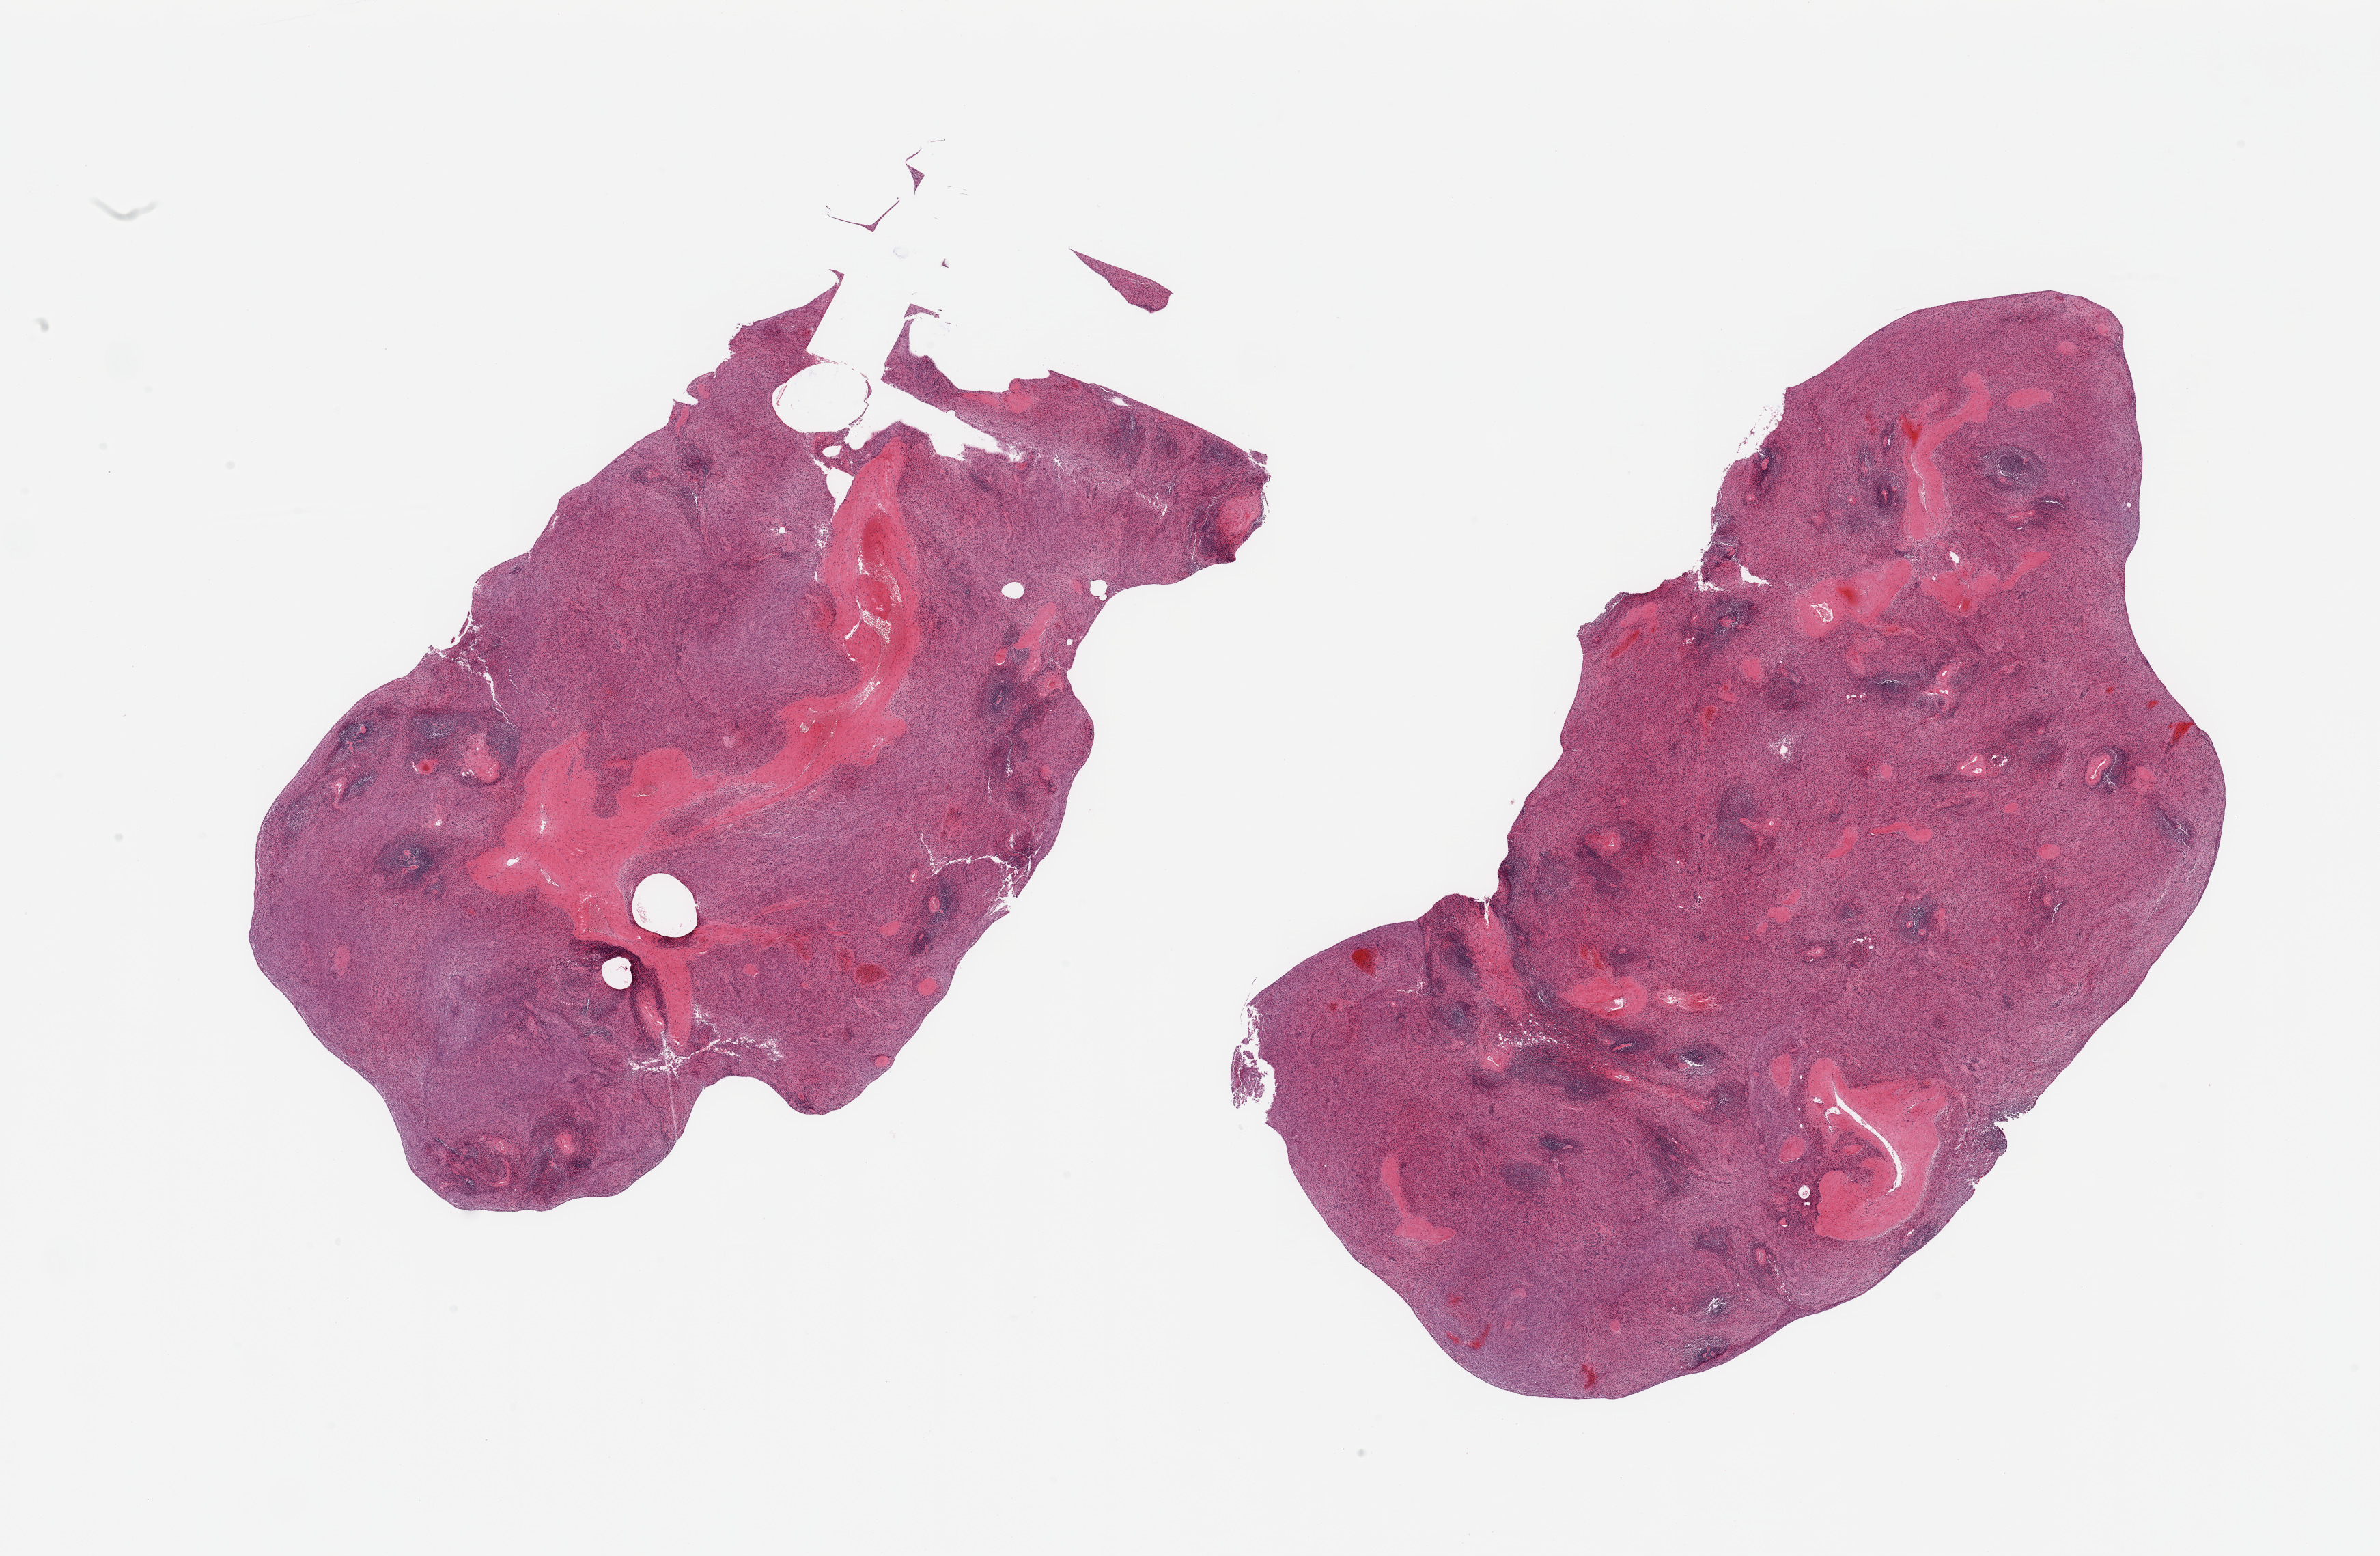
Digitized haematoxylin and eosin-stained section — whole scanned area (about 27.6 x 18.0 mm) shown as a low-resolution overview; PAXgene-fixed, paraffin-embedded tissue; sampled site (target tissue): spleen; donor tissue sample. Donor: male.
Pathologist's review note for this sample: 2 pieces; prominent thick-walled vessels.